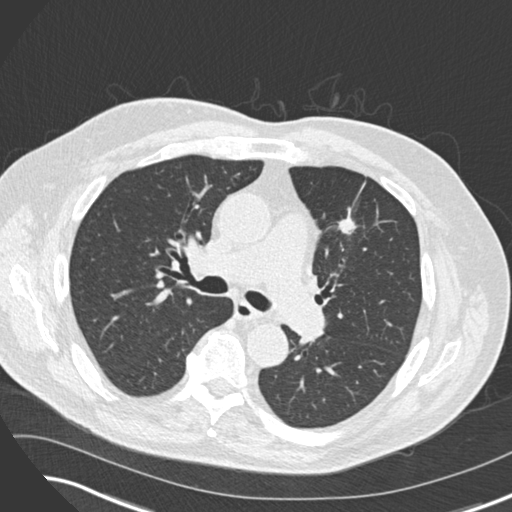
Low-dose screening chest CT, one axial slice. Slice 101 of 169 in the series (ordered by position). Lung window (W 1500 / L -600 HU). 512 × 512 image matrix, field of view 360 × 360 mm.
Outlined on this slice (manually delineated by an expert):
- lesion 1 (tumor, upper lobe of left lung): bounding box <339,213,356,234> (left, top, right, bottom; pixels)